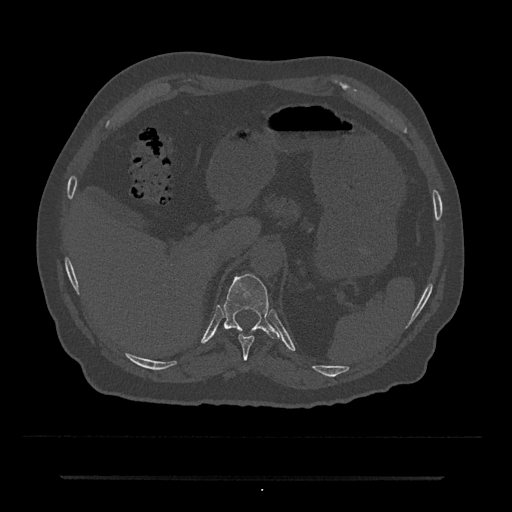
CT including the spine, one axial slice; slice 197 of 797 in the series (ordered by position); 120 kVp; bone window (W 1800 / L 400 HU); 0.5 mm slice thickness; 512 × 512 image matrix. Patient: male, 69 years. From the clinical record (not read from this slice): primary cancer: prostate.
Outlined on this slice (semi-automatically segmented with operator editing):
- T10 vertebra: bounding box <238,335,255,360> (left, top, right, bottom; pixels)
- T11 vertebra: <223,273,281,340>